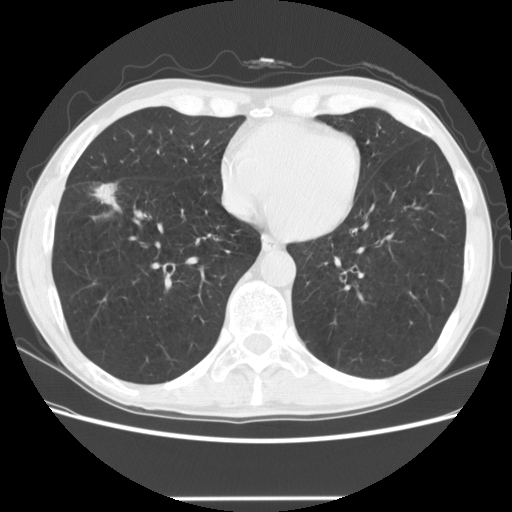
Low-dose screening chest CT, one axial slice; position 54 of 145 along the scan axis; lung window (W 1500 / L -600 HU); 2.5 mm slice thickness; 512 × 512 image matrix, field of view 365 × 365 mm.
Outlined on this slice (expert manual segmentation):
- lesion 1 (tumor, middle lobe of right lung): bounding box (x1, y1, x2, y2) in pixels: (94, 183, 121, 211)